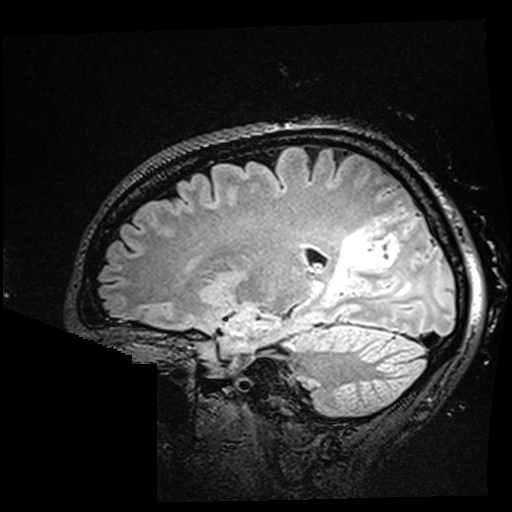
Brain MRI from a brain-tumour surgery series, one sagittal slice; slice 112 of 176 in the series (ordered by position); T2 FLAIR; 1 mm slice thickness; 512 × 512 image matrix. Case-level facts recorded for this patient, not image findings: histopathology: Oligodendroglioma; WHO grade: 2; IDH mutation: yes; tumour location: Right Parietal.
Annotated regions visible in this slice (outlined manually by an expert reader):
- residual tumour: bounding box (x1, y1, x2, y2) in pixels: (327, 230, 387, 294)